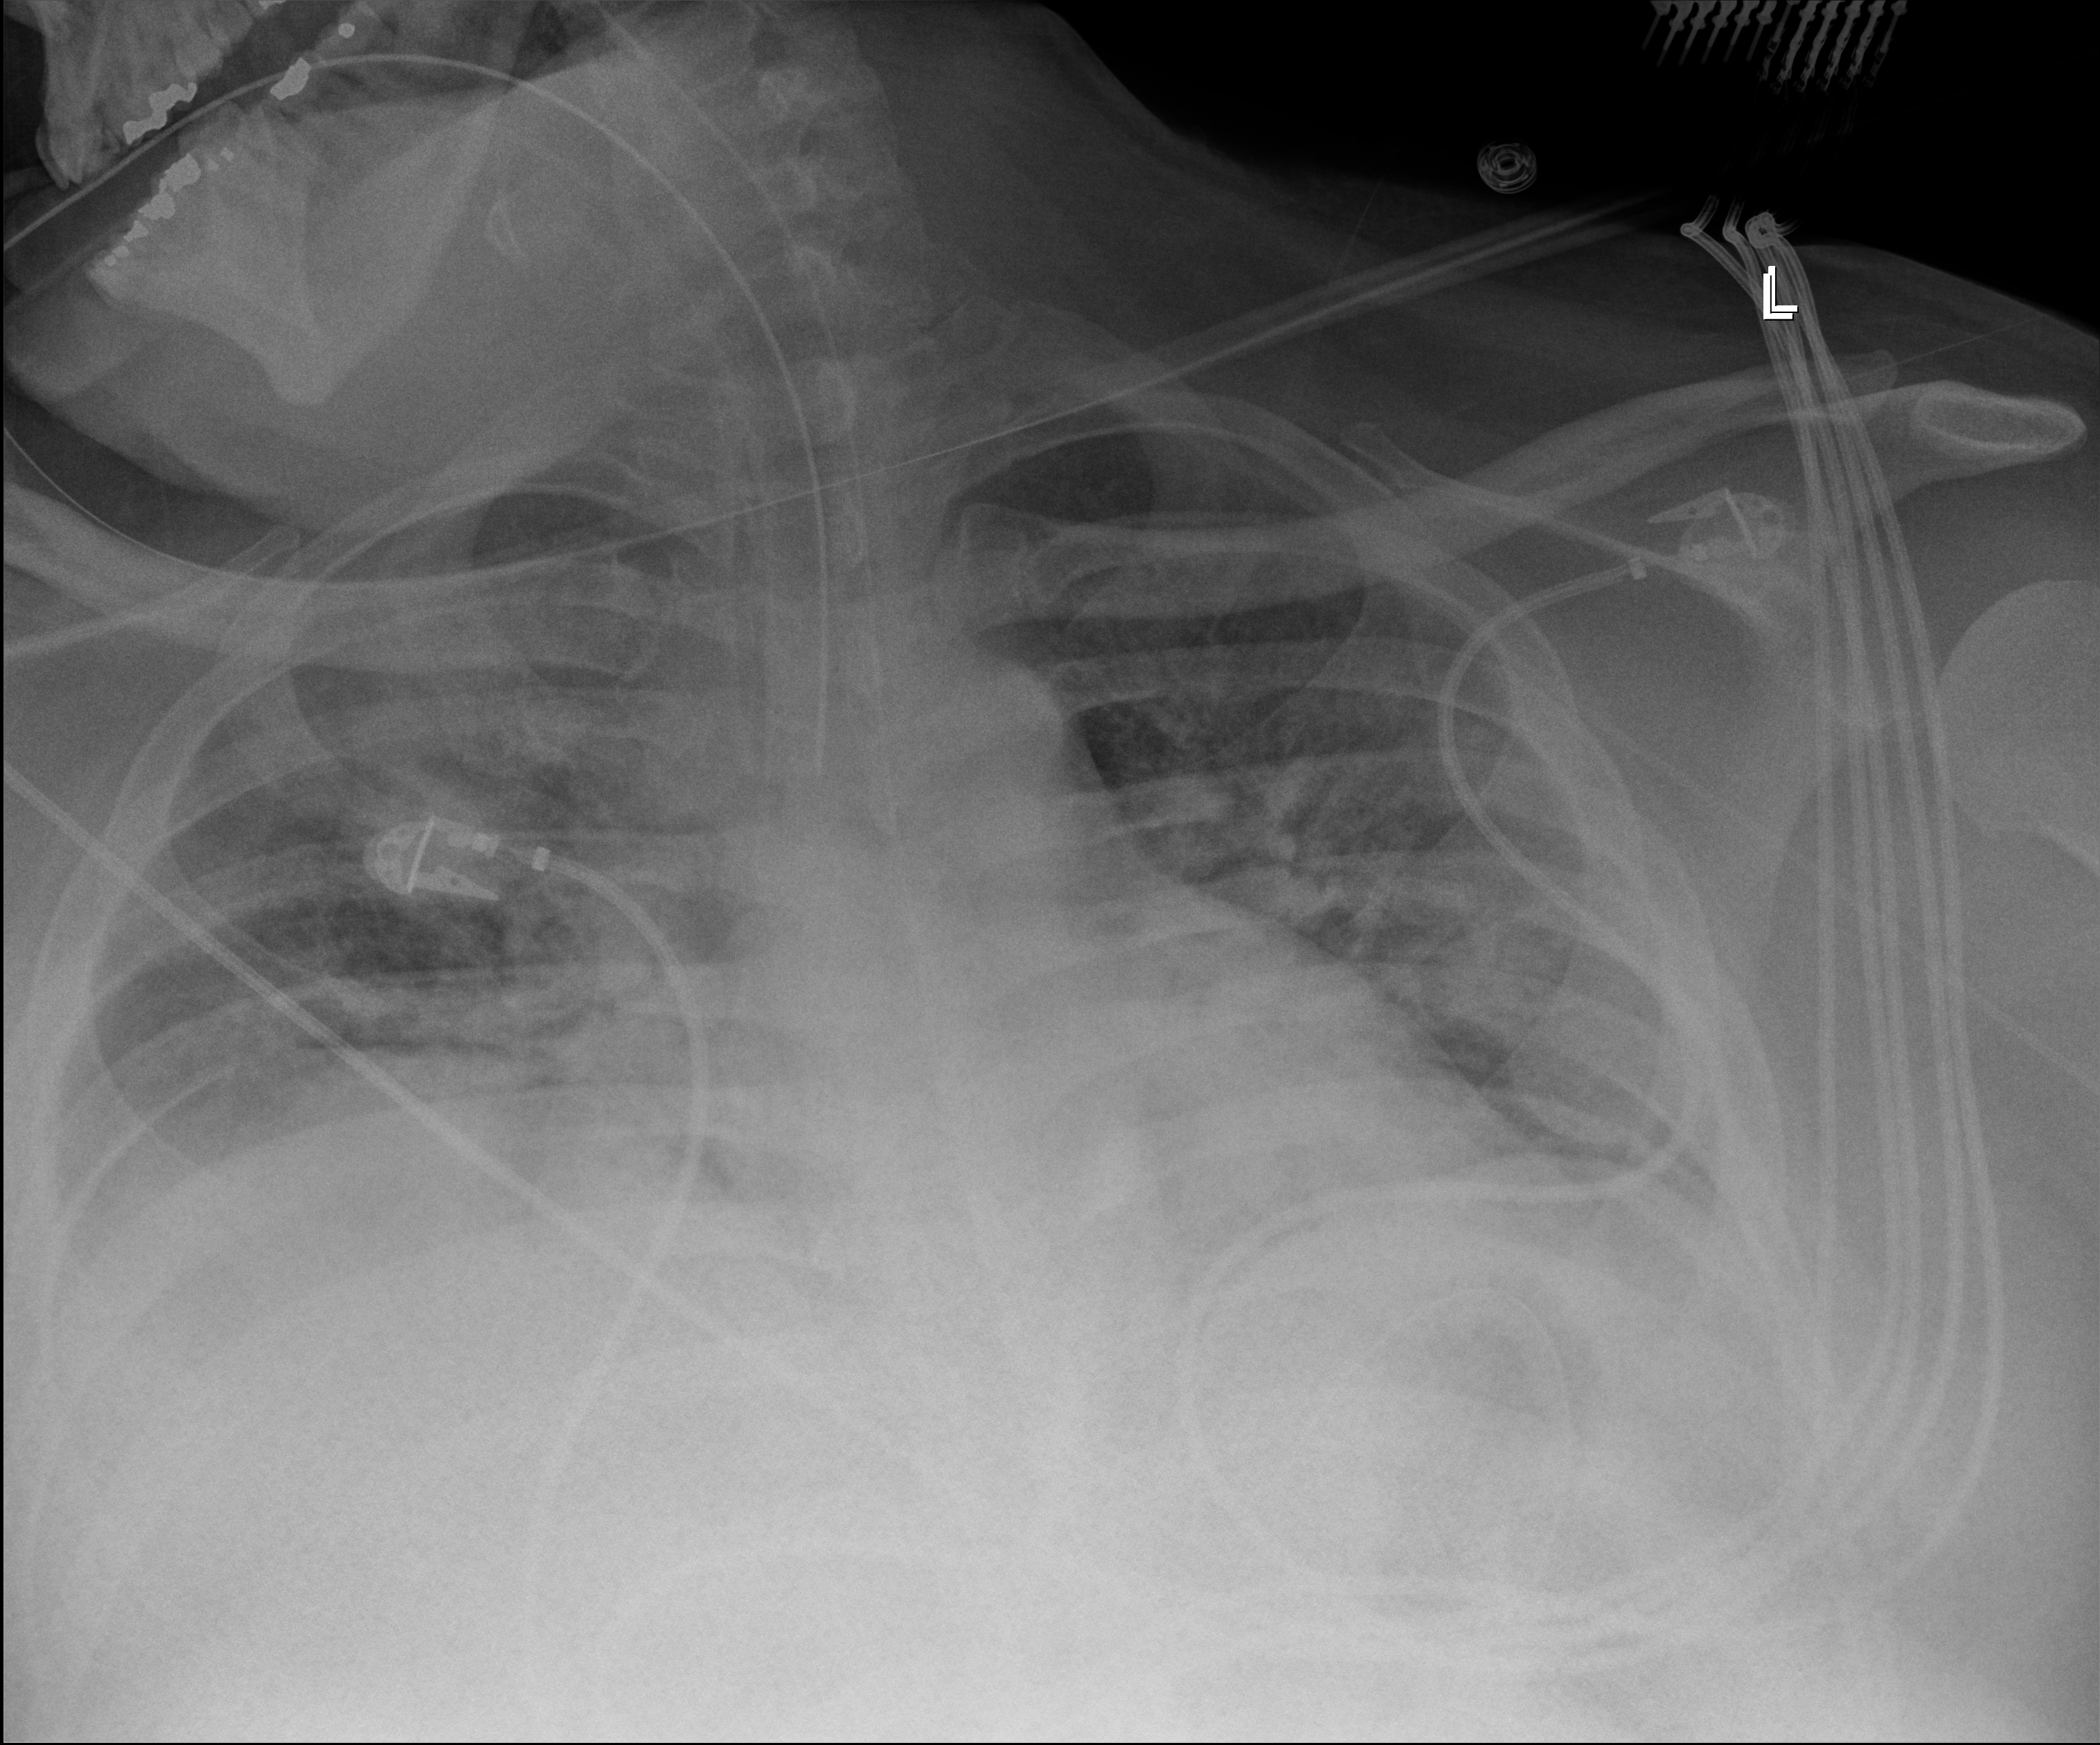
Portable chest radiograph, anteroposterior (AP) projection. Patient hospitalised with COVID-19; male, aged 18–59 years.
Hospital-stay facts (about this admission, not read from this image; timing relative to this image not recorded): hypertension (admission record): no; mechanically ventilated during this hospital stay: yes.